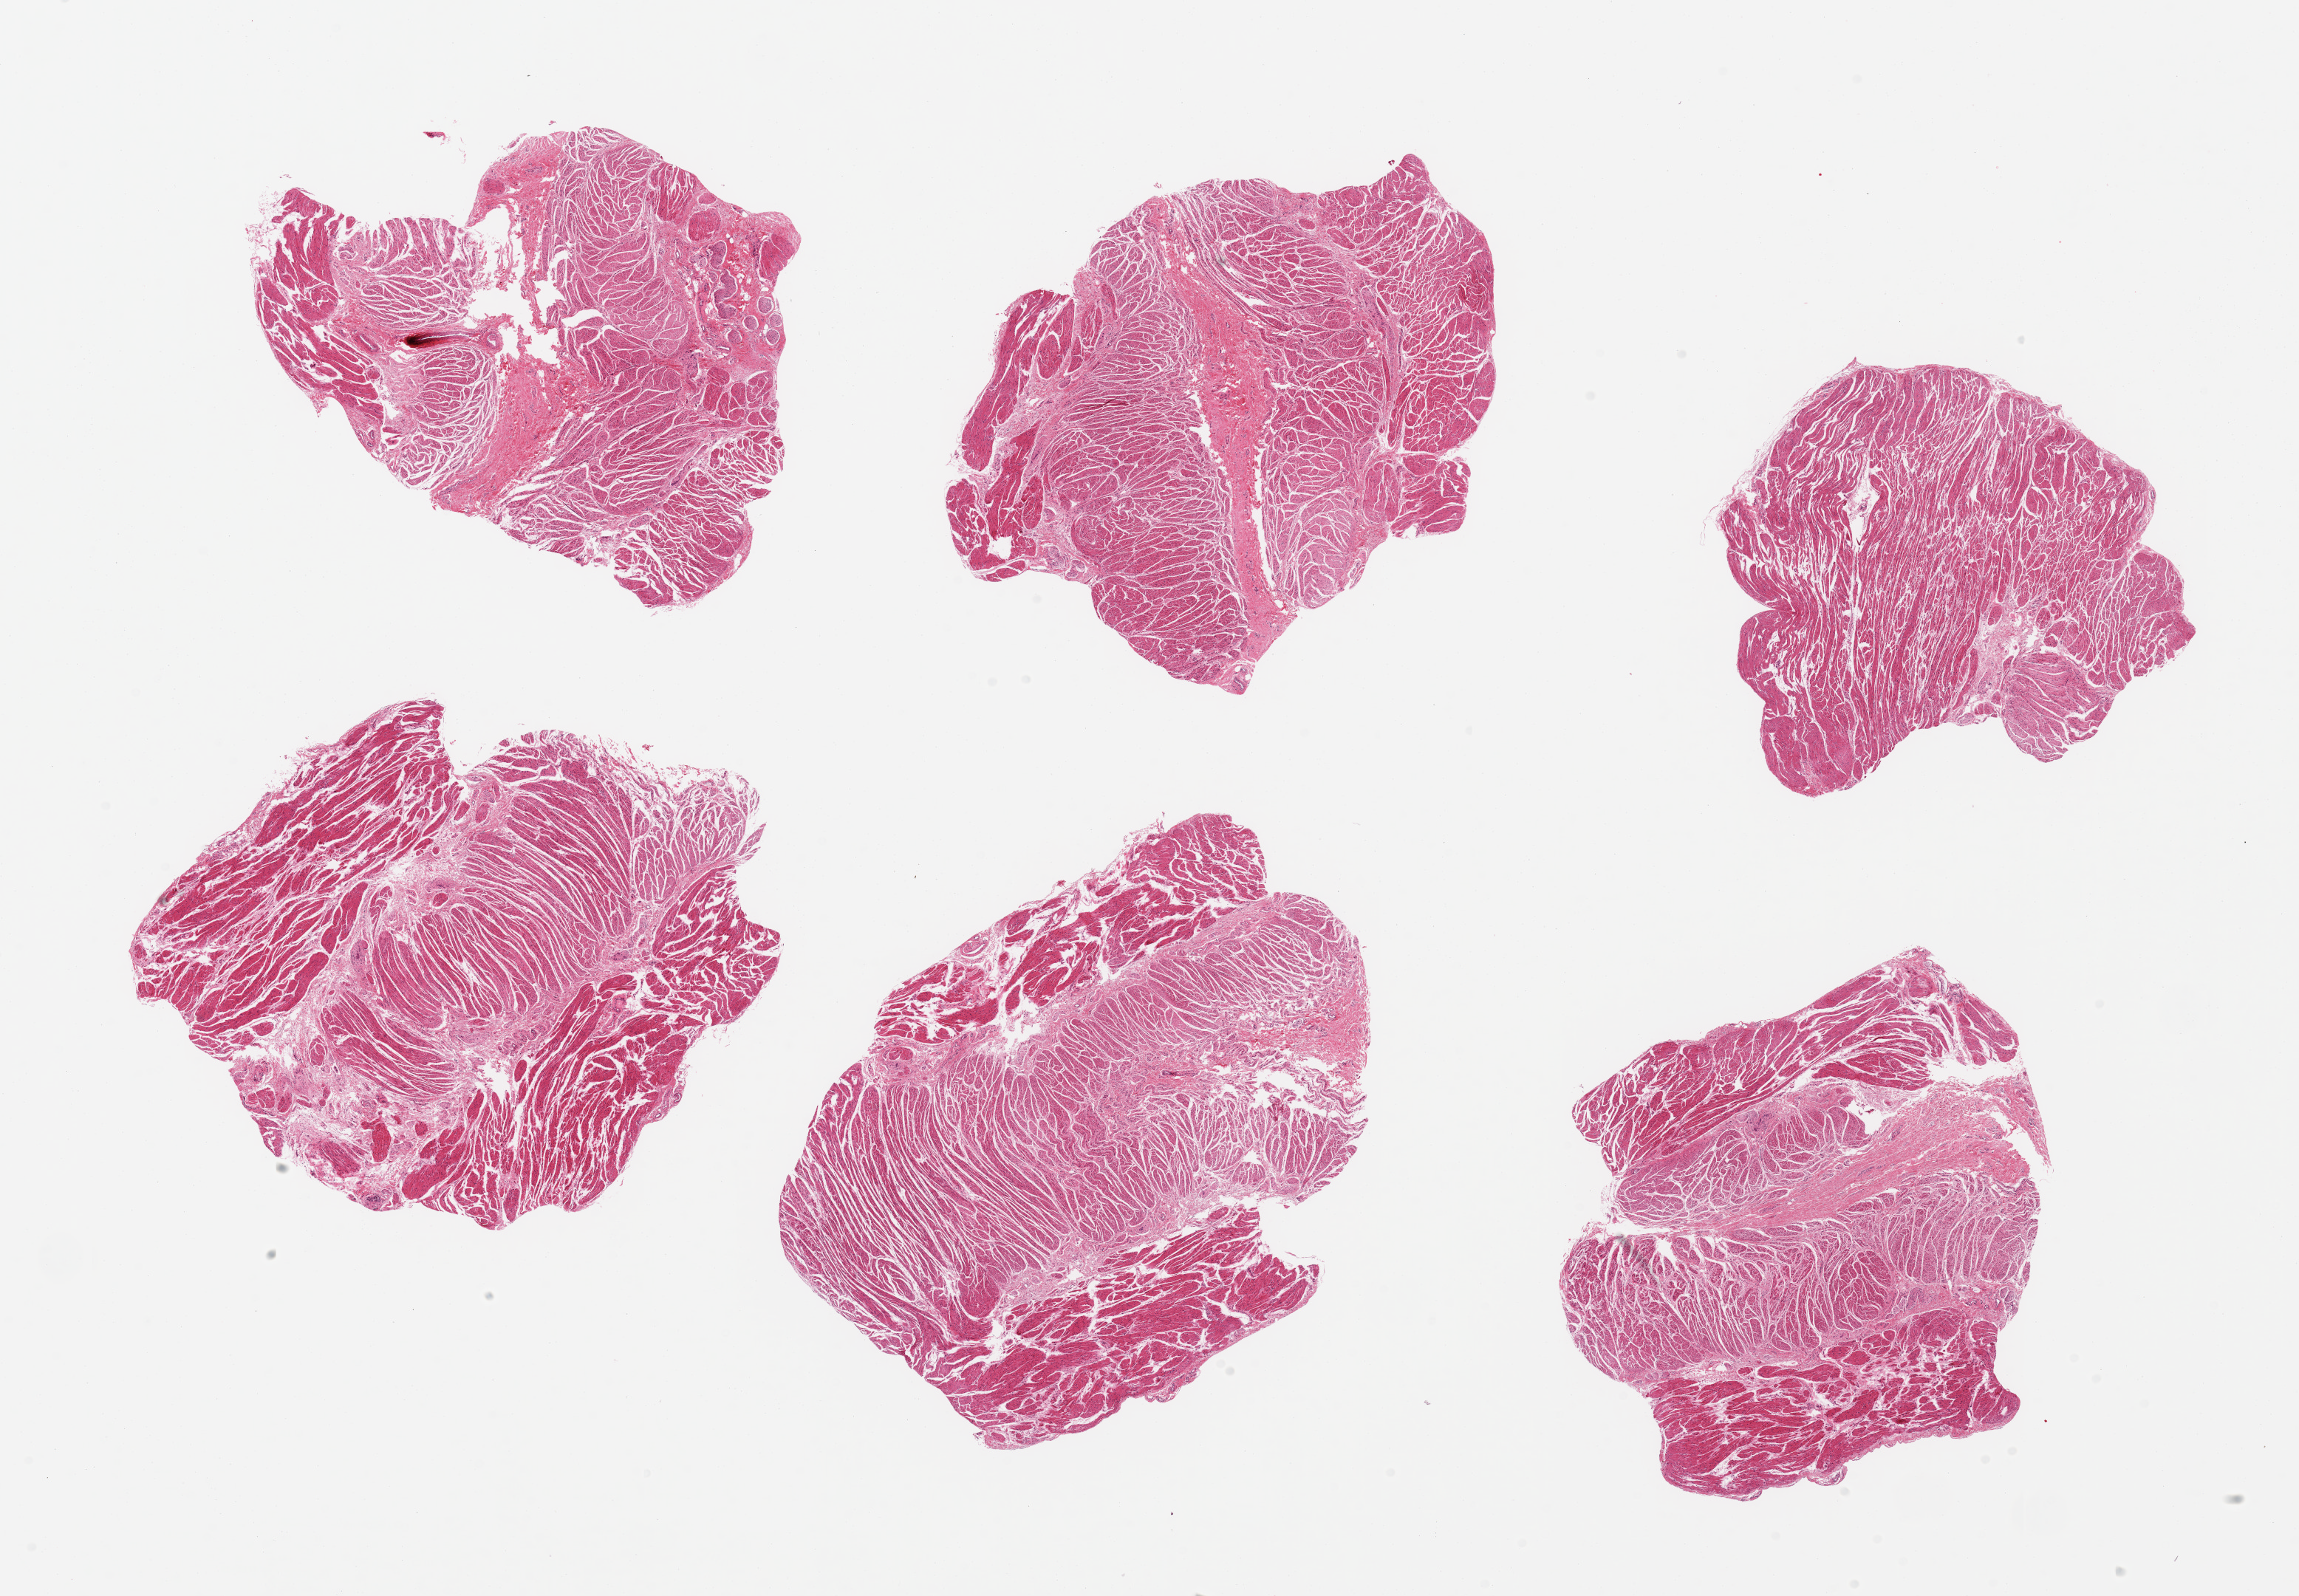
Digitized H&E-stained section — shown as a low-resolution overview of the whole scanned area (about 24.6 x 17.1 mm); PAXgene-fixed, paraffin-embedded tissue; target tissue: gastroesophageal junction; tissue donor sample. Donor: female.
- reviewer comment on this tissue sample: 6 pieces, confirmed target muscularis